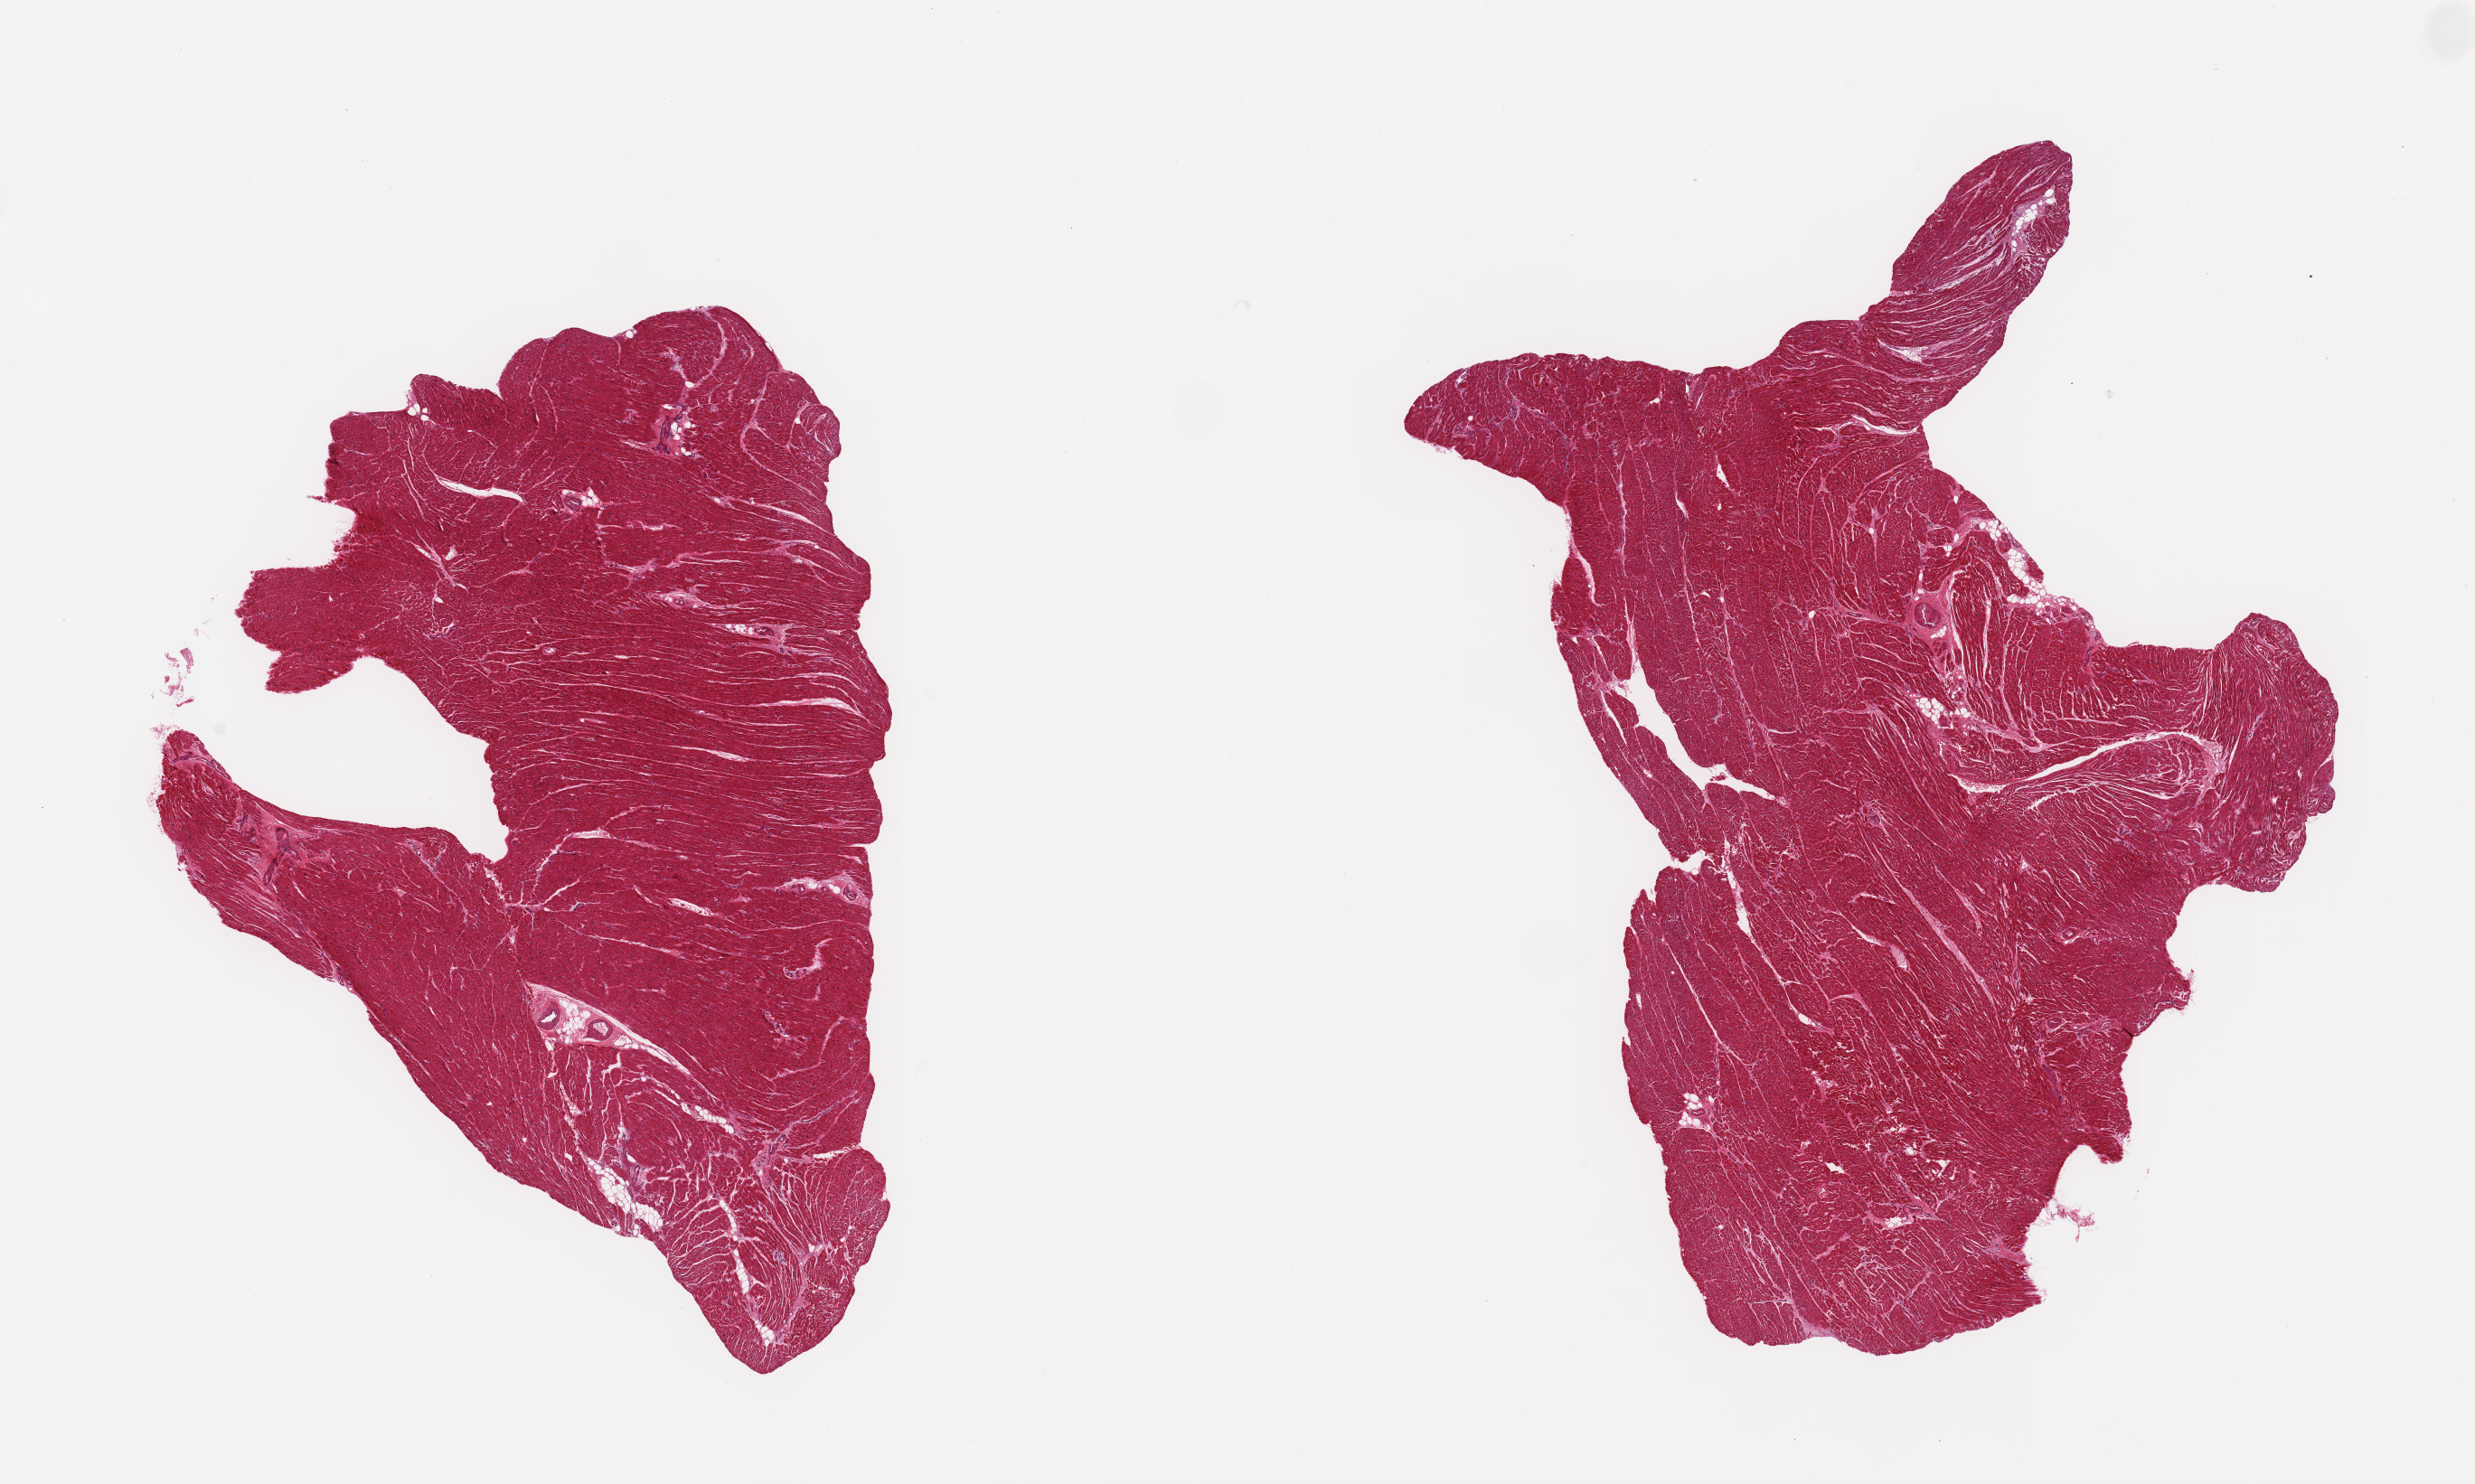
Digitized haematoxylin and eosin-stained section, low-resolution overview of the scanned area, about 21.7 x 13.0 mm (slide scanned at 20x), PAXgene-fixed paraffin-embedded (PFPE) section, sampled site (target tissue): heart, tissue donor sample. Male donor.
Review note (as recorded): 2 pieces; minimal fibrous & fatty content.